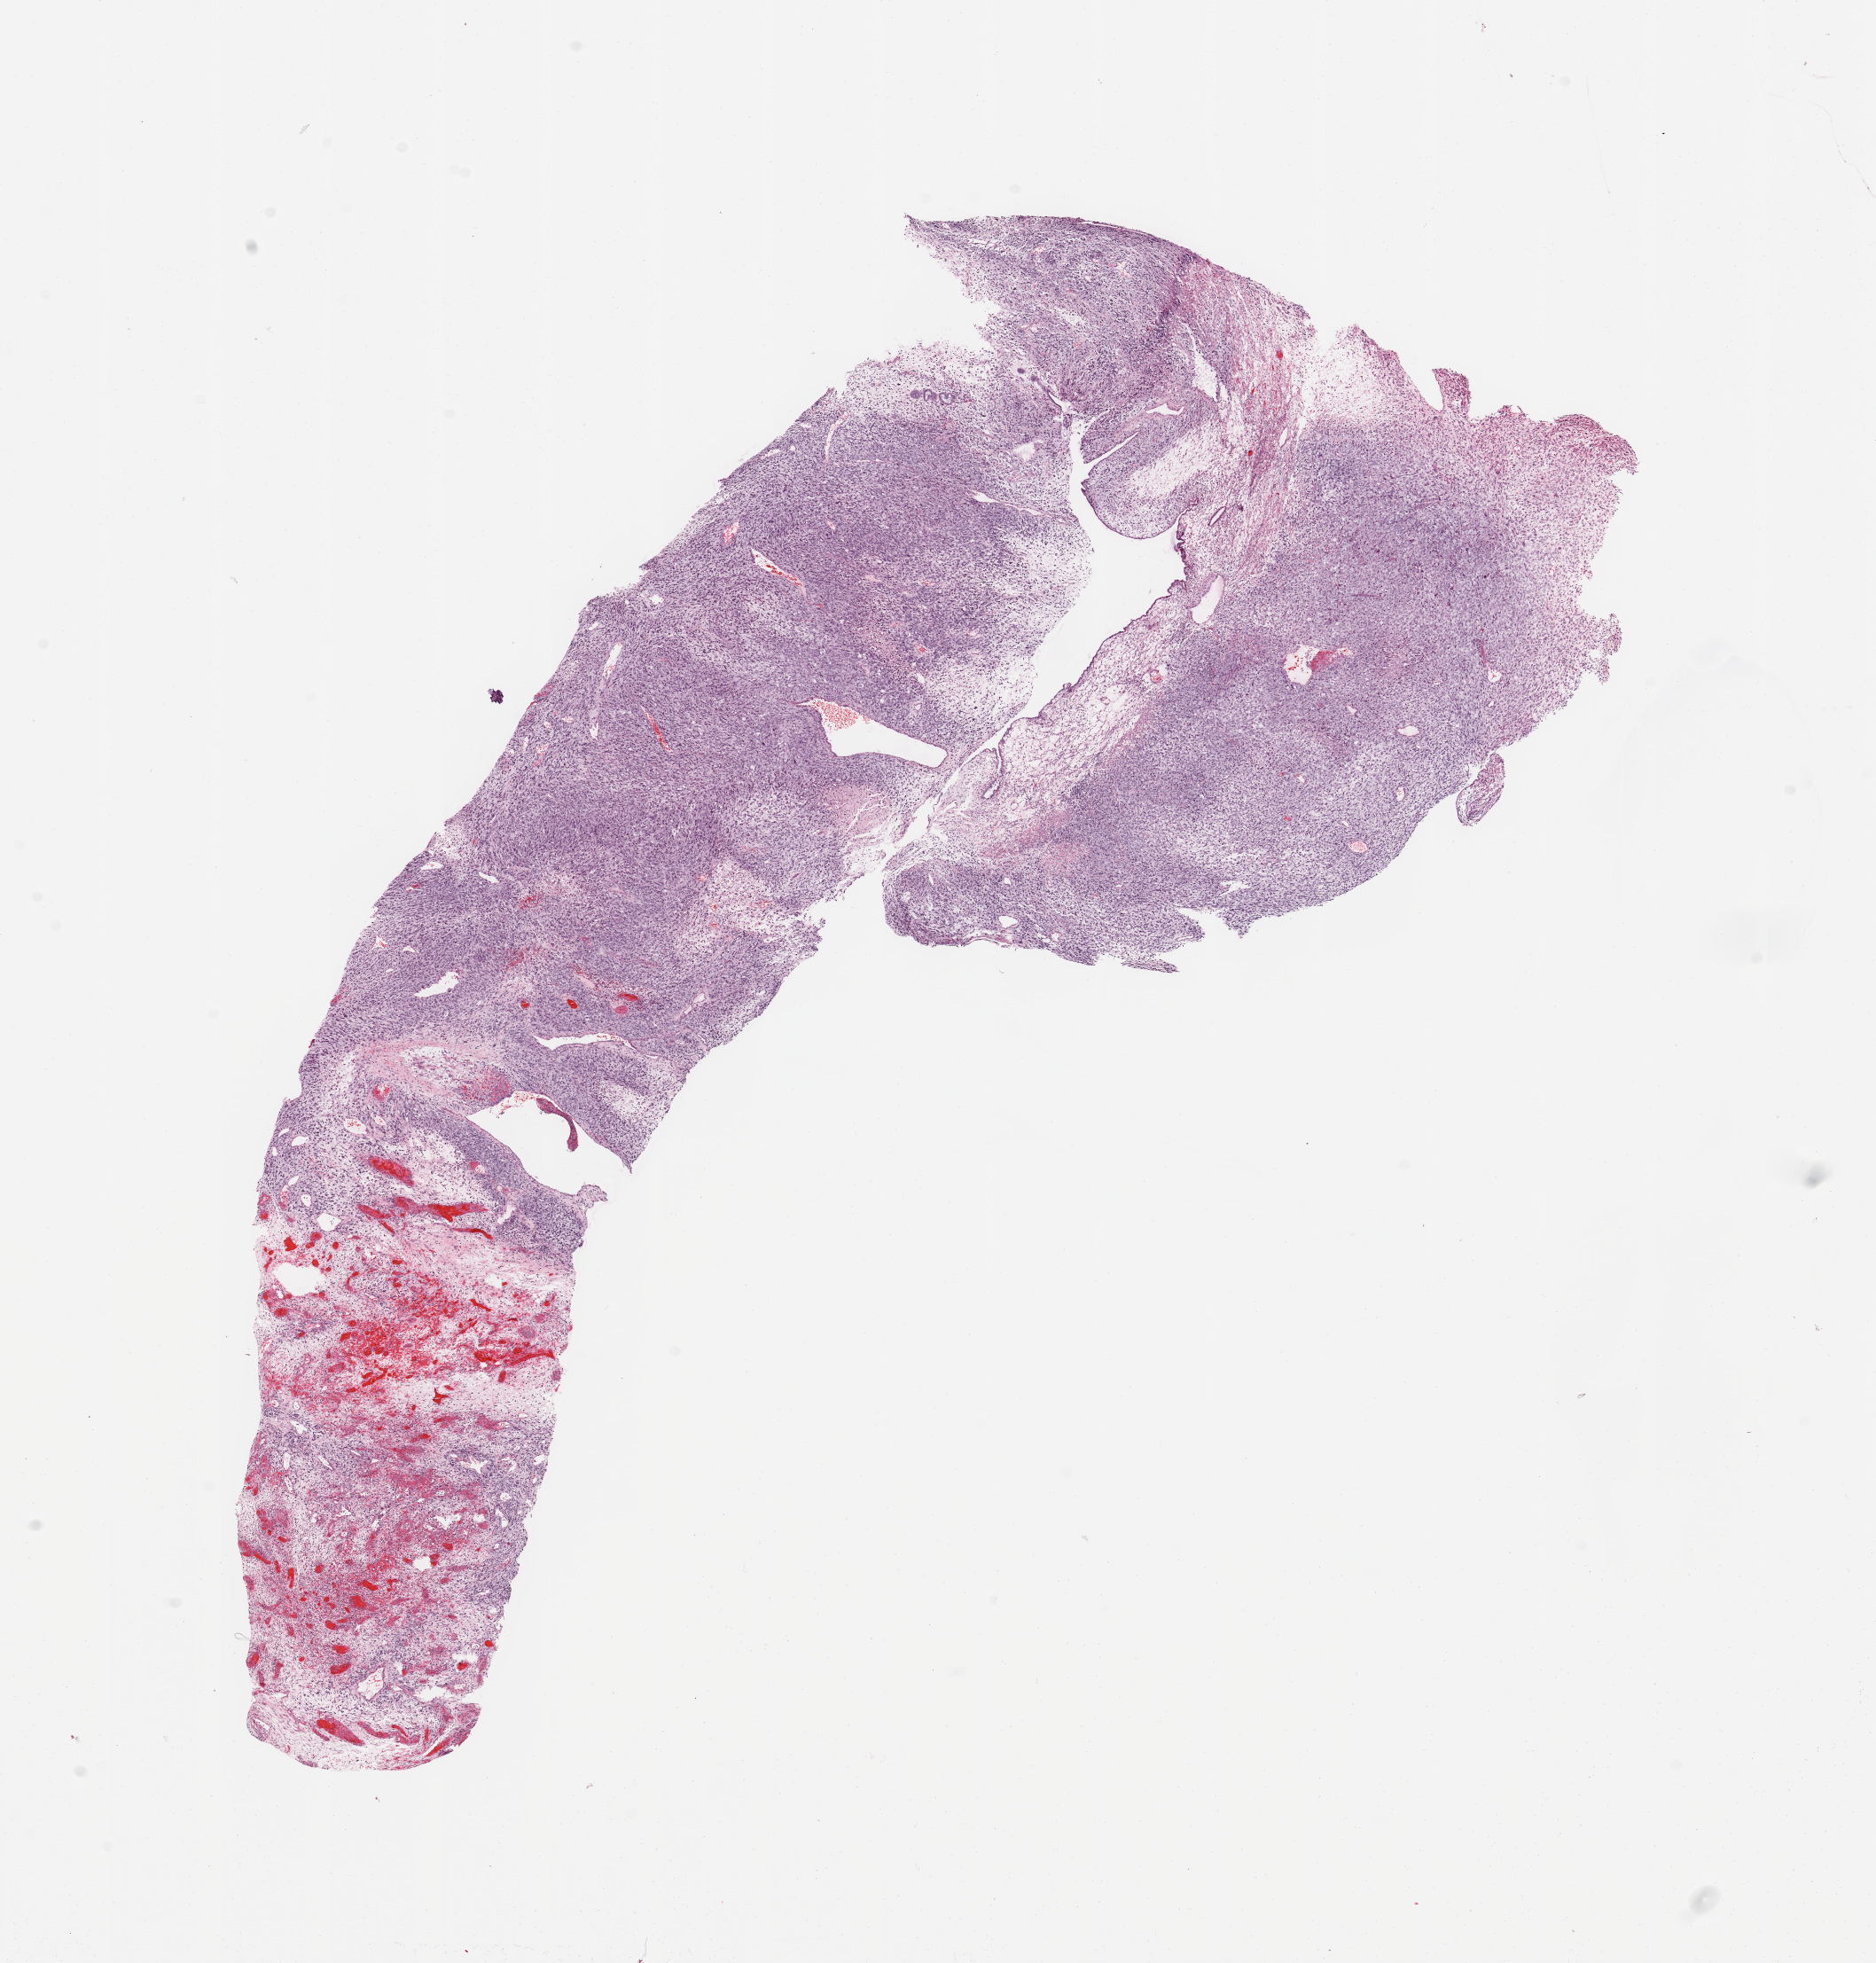
Digitized H&E tissue section (whole slide) — shown as a low-resolution overview of the whole scanned area (about 16.7 x 17.5 mm). Patient: female, age 62 years.
Patient diagnosis (cohort enrolment): sarcoma (site not recorded at cohort level). Primary tumour site (as recorded): gynecologic.